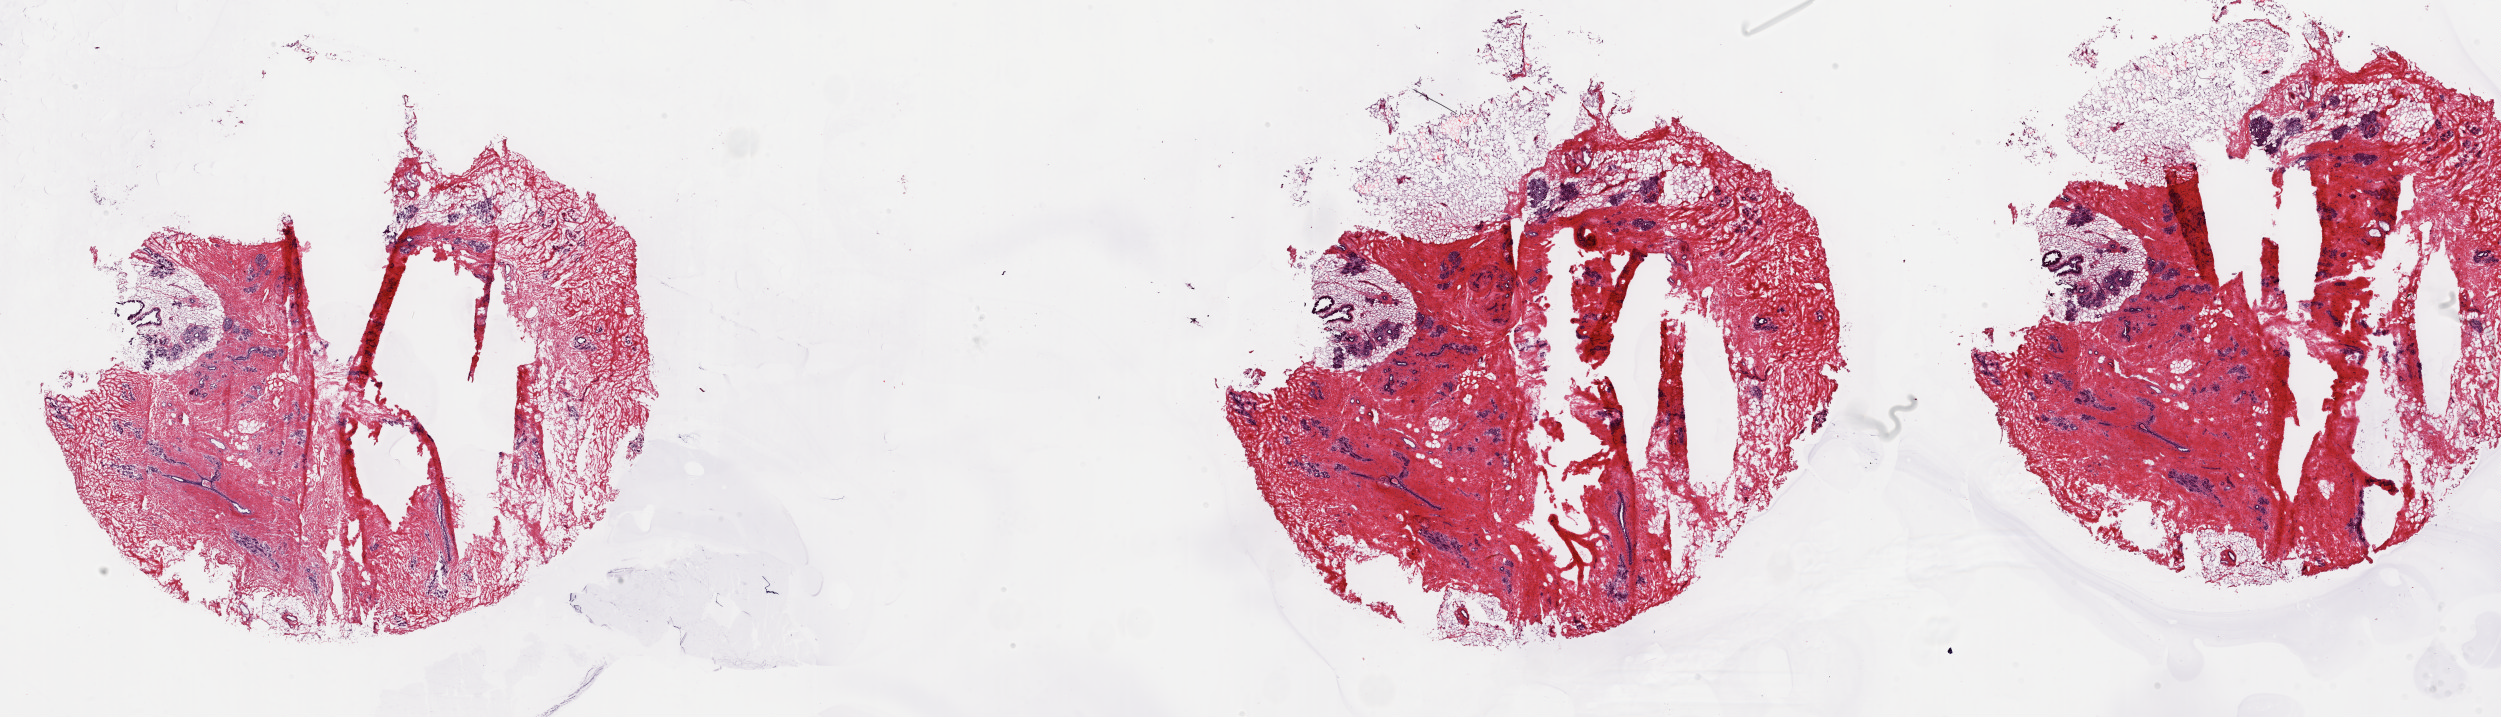
Whole-slide histology image, H&E-stained, a low-resolution overview of the entire scanned area, about 39.7 x 11.4 mm; frozen section from the top of the tissue portion; sample: solid tissue normal (non-tumour tissue), breast. Female patient; age at initial diagnosis 40 years. Composition of this section per pathologist review: tumour cells 0%, tumour nuclei 0%, normal cells 100%, stromal cells 0%, necrosis 0%. Inflammatory infiltration, as recorded: lymphocyte infiltration 1%, monocyte infiltration 0%, neutrophil infiltration 0%.
This section: solid tissue normal (non-tumour) sample from the same patient. Patient diagnosis: Lobular carcinoma, NOS.